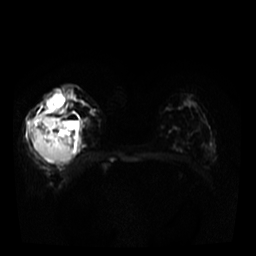
Breast MRI, one axial slice. Diffusion-weighted series; image 2 of 4 stored at this slice position (different b-values; order by instance number). 3 T. 5 mm slice thickness. 256 × 256 image matrix. Female patient.
Outlined on this slice (expert manual segmentation):
- tumour on diffusion-weighted imaging: bounding box [x1, y1, x2, y2] px = [31, 117, 76, 163]